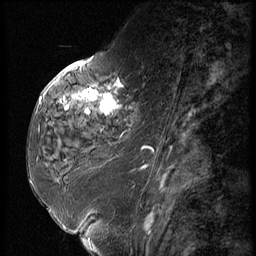
Breast MRI (dynamic contrast-enhanced), one sagittal slice; slice 23 of 56 in the series (ordered by position); dynamic contrast-enhanced series, image 2 of 3 at this slice position (ordered by acquisition); 1.5 T; TE 4.2 ms, TR 9 ms; 256 × 256 image matrix, field of view 180 × 180 mm. Female patient, age 59 years. From the clinical record (not read from this slice): setting: breast cancer imaged before/during neoadjuvant chemotherapy; receptor status: HER2-positive.
Annotated regions visible in this slice (semi-automatic segmentation, software-assisted and operator-edited):
- analysis volume of interest (the breast-tissue region the enhancement analysis was run in; not a lesion): bounding box <44,66,145,135> (left, top, right, bottom; pixels)
- tumour enhancement mask (voxels above the 140 % enhancement threshold inside the analysis volume of interest): <63,78,131,114>